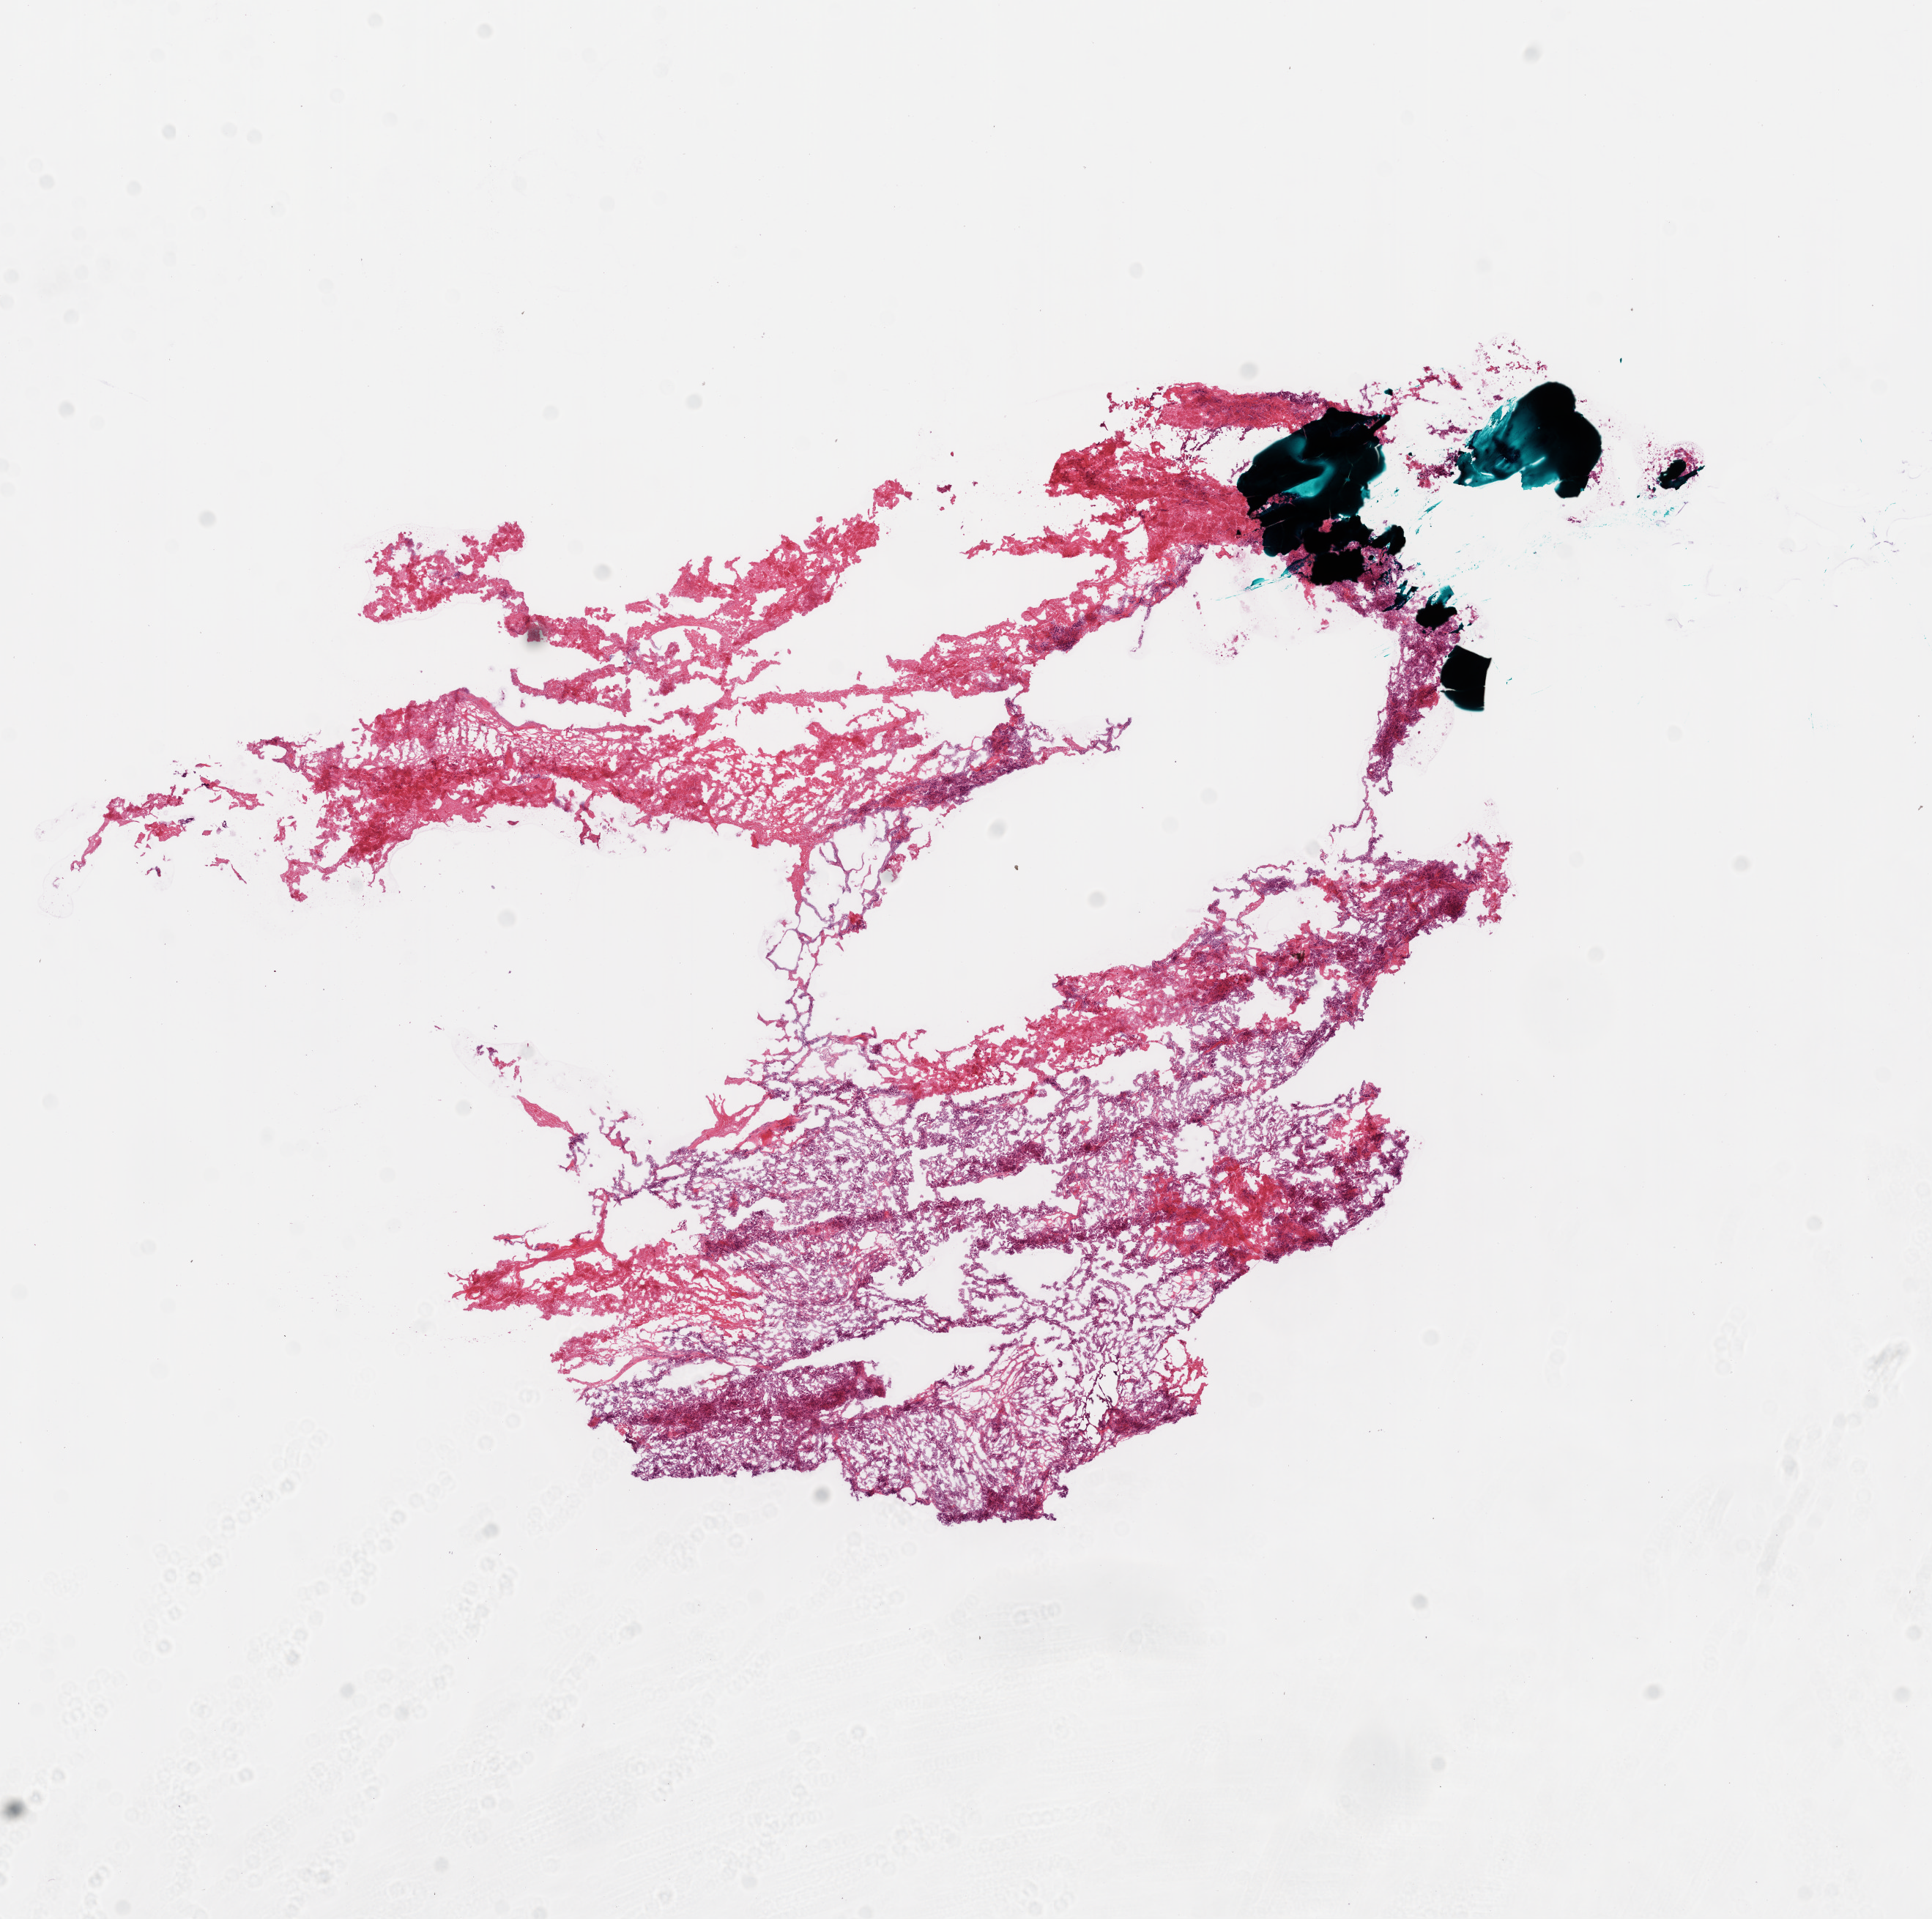
Digitized H&E-stained tissue section (whole slide) — low-resolution overview of the scanned area, about 10.6 x 10.6 mm. Frozen section. Ovary, primary tumour sample. Female, age 60 years at initial diagnosis. Histologic grade: G3 (poorly differentiated). Slide review estimates, as recorded: tumour cells 75%, tumour nuclei 85%, normal cells 5%, stromal cells 5%, necrosis 15%.
FIGO stage: IV. Pathologic diagnosis: Serous cystadenocarcinoma, NOS.